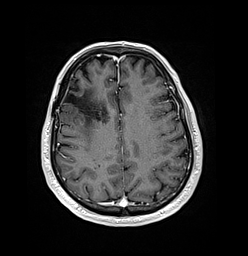
Brain MRI from a brain-tumour surgery series, one axial slice; slice 56 of 176 in the series (ordered by position); T1-weighted post-contrast; 1 mm slice thickness; 248 × 256 image matrix, field of view 242 × 250 mm. Case-level facts recorded for this patient, not image findings: histopathology: Oligodendroglioma; WHO grade: 3; IDH mutation: yes; tumour location: Right Frontal.
Annotated regions visible in this slice (manually delineated by an expert):
- previous resection cavity: bounding box (x1, y1, x2, y2) in pixels: (64, 93, 79, 106)
- tumour: (73, 119, 83, 127)